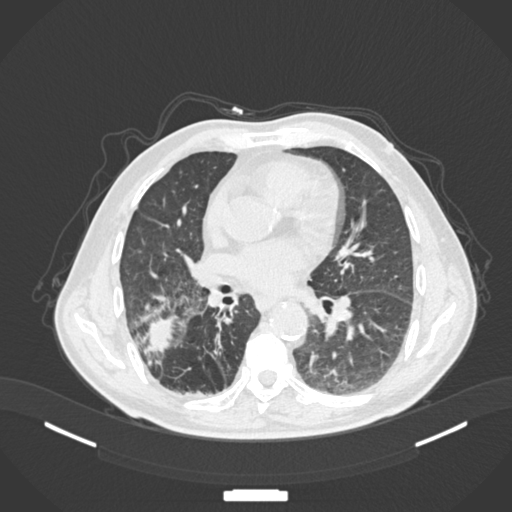
Chest CT, one axial slice. Slice 76 of 201 in the series (ordered by position). 120 kVp. Lung window (W 1500 / L -600 HU). 1 mm slice thickness. 512 × 512 image matrix. Patient: male, 72 years. From the clinical record (not read from this slice): clinical TNM (as recorded): T3 N2 M0.
Structures marked on this image (bounding box drawn by a radiologist):
- lung tumour (recorded histology: adenocarcinoma): bounding box [x1, y1, x2, y2] px = [145, 311, 180, 357]